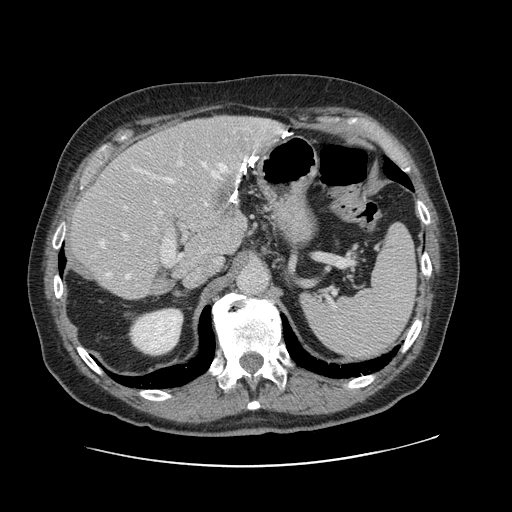
Contrast-enhanced abdominal CT, one axial slice. Slice 77 of 138 in the series (ordered by position). 120 kVp. Soft-tissue window (W 400 / L 40 HU). 2.5 mm slice thickness. 512 × 512 image matrix, field of view 402 × 402 mm. Male patient, age 71 years. From the clinical record (not read from this slice): diagnosis: colorectal cancer liver metastases, imaged before liver resection; multiple liver metastases: no; largest metastasis: 3.3 cm.
Outlined on this slice (expert manual segmentation):
- hepatic veins: bounding box [x1, y1, x2, y2] px = [100, 153, 256, 279]
- liver: [71, 117, 283, 300]
- planned liver remnant (the part of the liver to remain after resection): [71, 149, 234, 299]
- portal vein (with intrahepatic branches): [122, 160, 184, 263]
- liver metastasis: [210, 180, 238, 218]